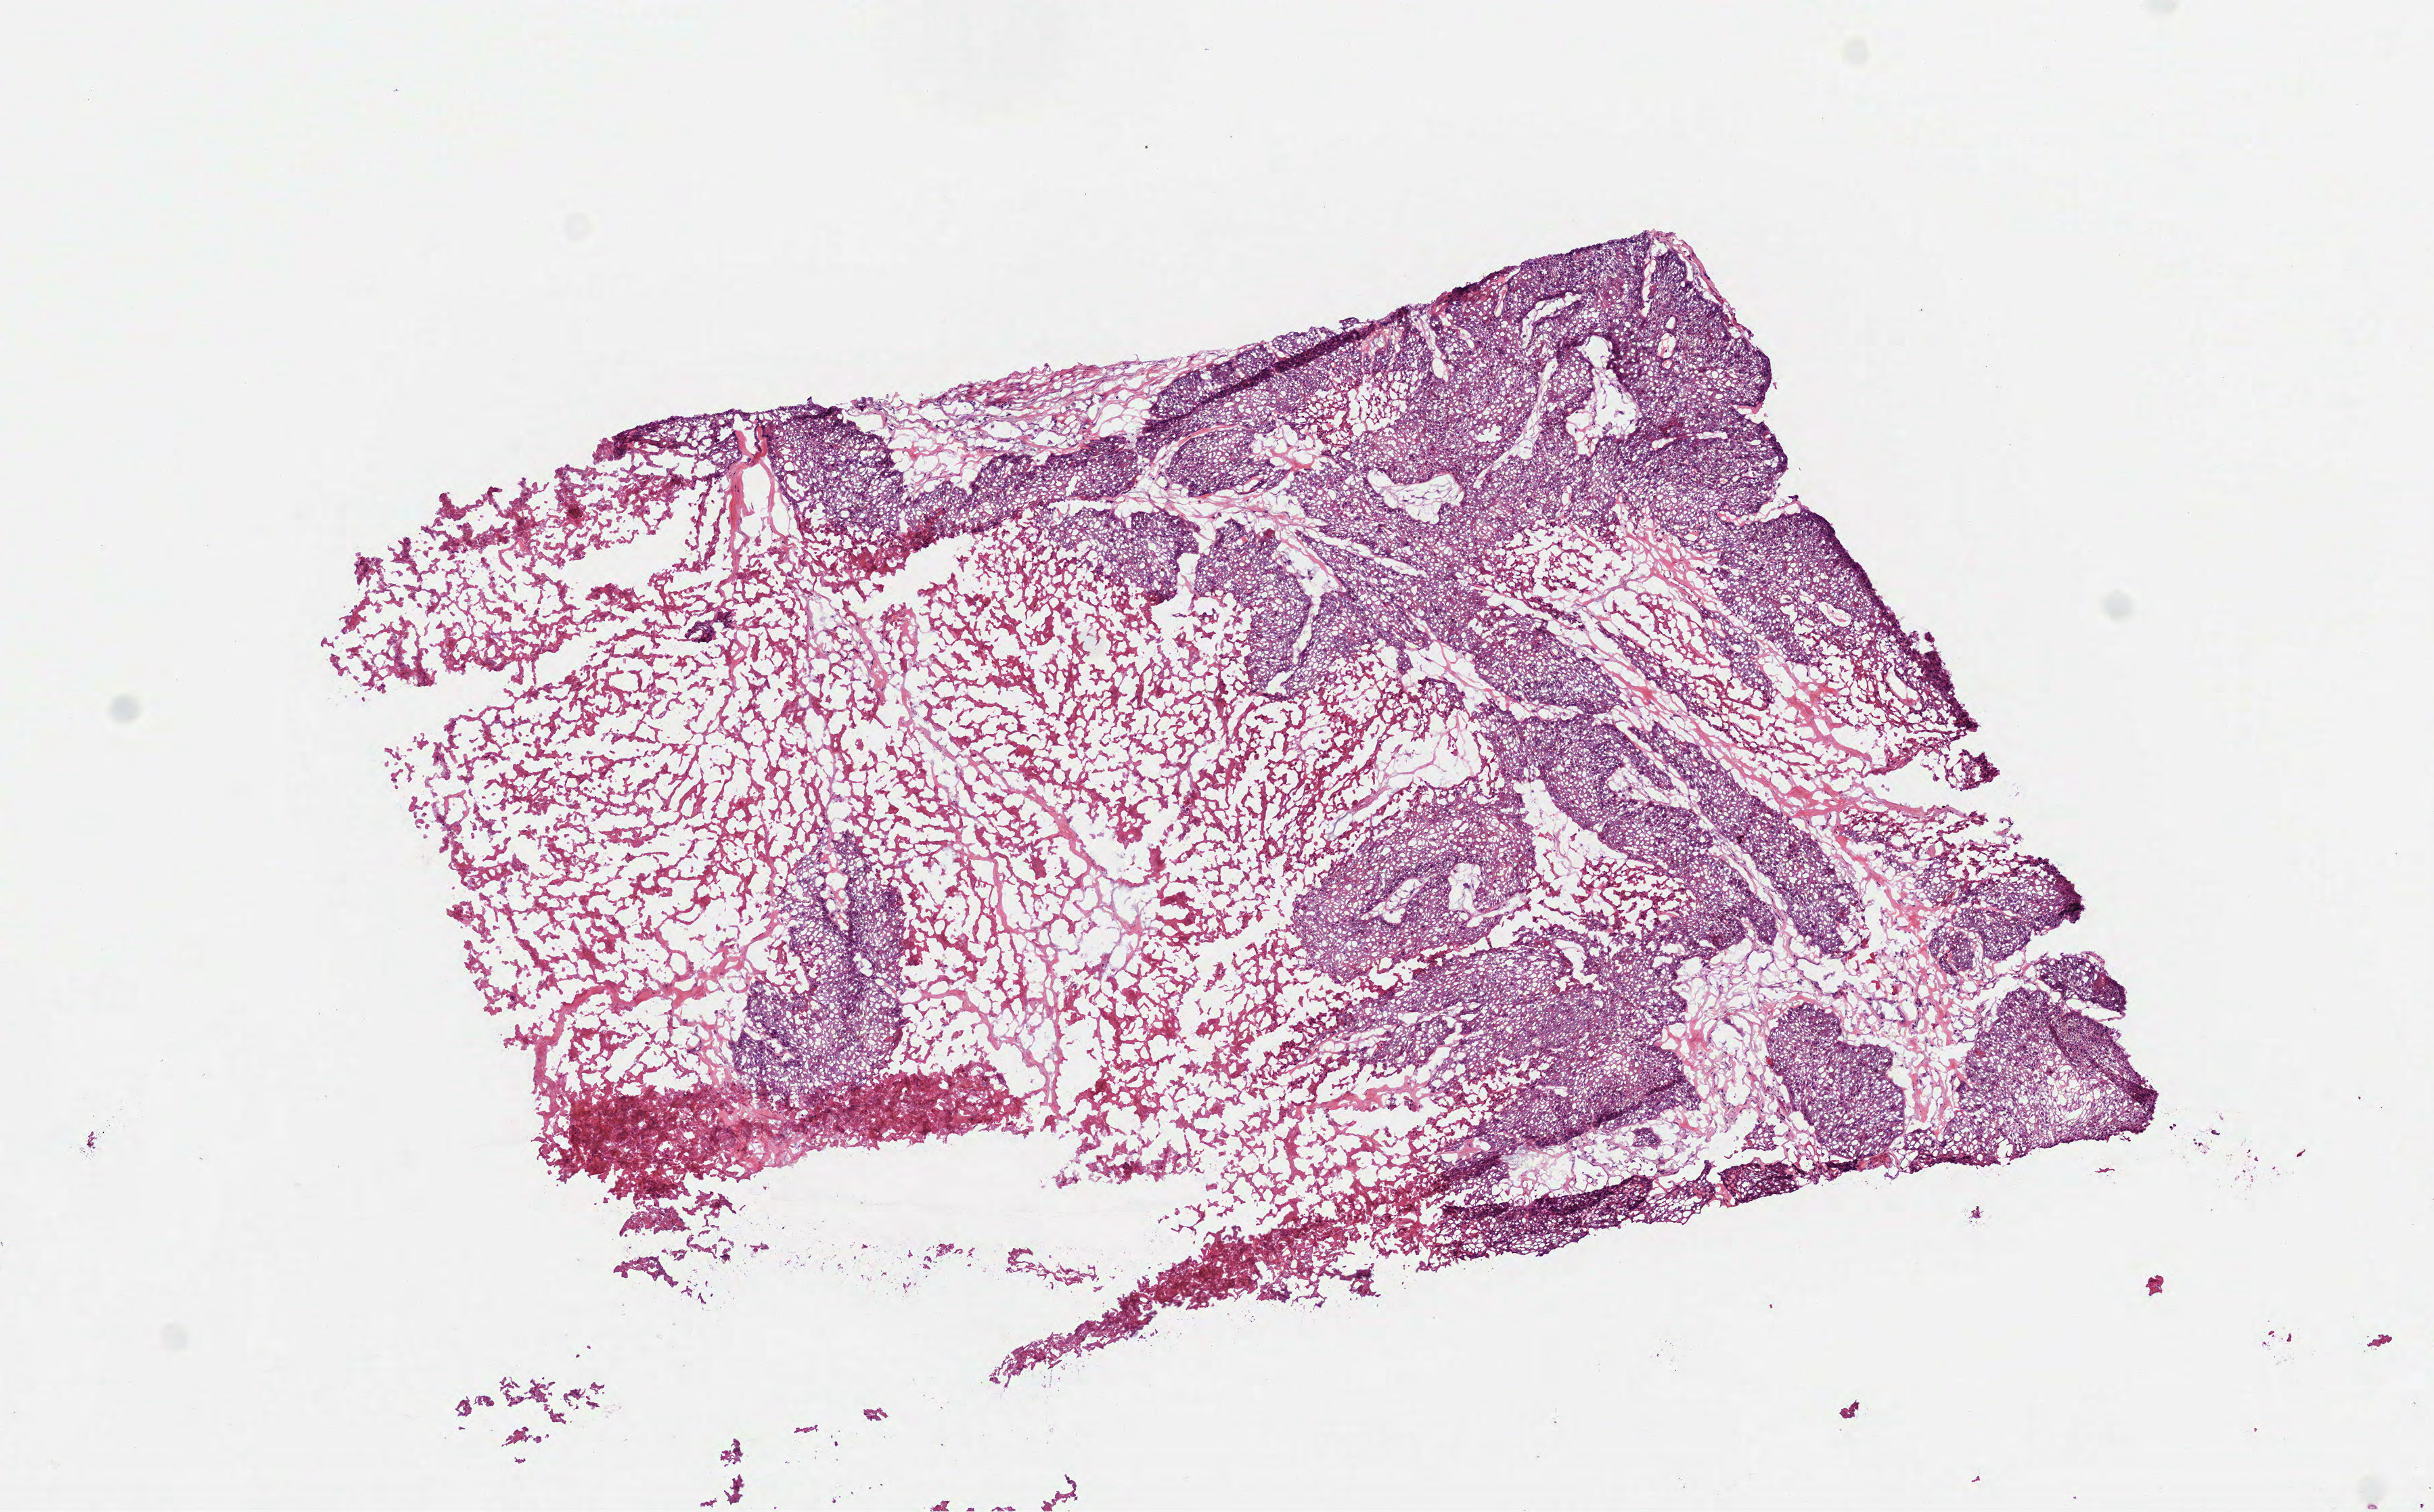
Whole-slide histology image, Hematoxylin and eosin (H&E) stained — whole scanned area (about 7.3 x 4.5 mm, from a 40x scan) shown as a low-resolution overview. Frozen section from the top of the tissue portion. Sample: primary tumour, head and neck. Male patient; age at initial diagnosis 58 years. Histologic grade: G2 (moderately differentiated). Pathologist review of this section (percent, as recorded): tumour cells 40%, tumour nuclei 85%, normal cells 0%, stromal cells 60%, necrosis 0%.
* pathologic diagnosis: Squamous cell carcinoma, NOS
* AJCC pathologic stage: IVA (7th edition)